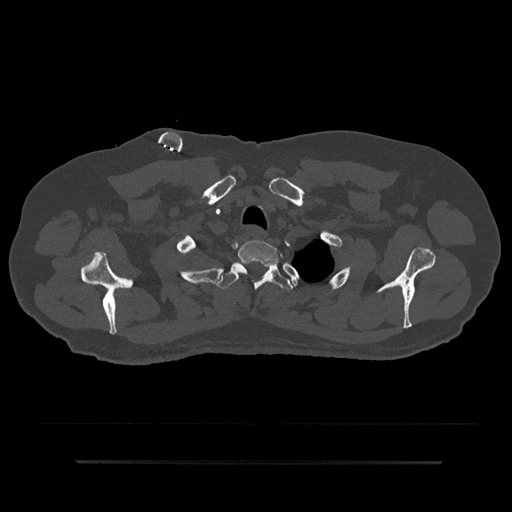
CT including the spine, one axial slice. Slice 714 of 797 in the series (ordered by position). Bone window (W 1800 / L 400 HU). 0.5 mm slice thickness. 512 × 512 image matrix, field of view 464 × 464 mm. Patient: male, 59 years. Case-level facts recorded for this patient, not image findings: primary cancer: bile ducts; vertebrae with lytic lesions (as recorded): T10.
Annotated regions visible in this slice (semi-automatically segmented with operator editing):
- T1 vertebra: box from (x=234, y=240) to (x=279, y=275) px
- T2 vertebra: (x=216, y=262)–(x=293, y=291)